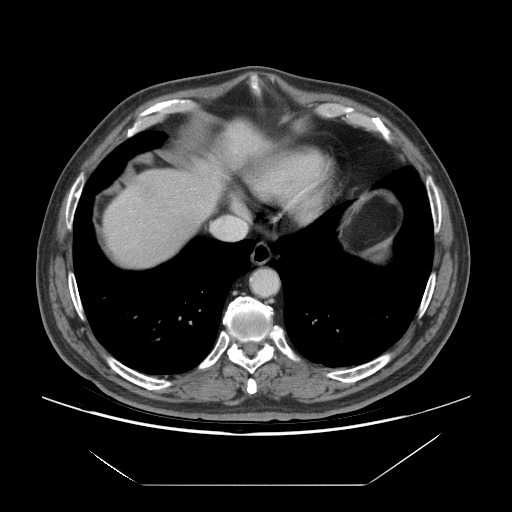
Contrast-enhanced abdominal CT (liver protocol), one axial slice. Position 64 of 75 along the scan axis. 140 kVp. Soft-tissue window (W 400 / L 40 HU). 512 × 512 image matrix. Case-level facts recorded for this patient, not image findings: diagnosis: hepatocellular carcinoma (patient treated with transarterial chemoembolisation; whether this scan precedes or follows treatment is not stated here); TNM stage (as recorded): Stage-I; Child-Pugh class: A; tumour differentiation: well differentiated; tumour nodularity: uninodular.
Outlined on this slice (semi-automatically segmented with operator editing):
- liver parenchyma outside the tumour (the mass and vessels are separate outlines, so this box may not span the whole liver): bounding box (x1, y1, x2, y2) in pixels: (104, 122, 286, 266)